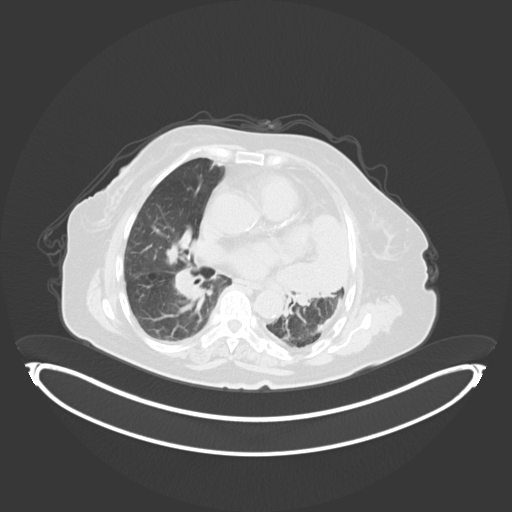
Chest CT, one axial slice; position 195 of 284 along the scan axis; reconstruction kernel B30f; 120 kVp; lung window (W 1500 / L -600 HU); 512 × 512 image matrix, field of view 500 × 500 mm. Patient: female, 75 years. From the clinical record (not read from this slice): clinical TNM (as recorded): T3 N3 M1.
Annotated regions visible in this slice (bounding box drawn by a radiologist):
- lung tumour (recorded histology: adenocarcinoma): bounding box (x1, y1, x2, y2) in pixels: (273, 201, 357, 305)